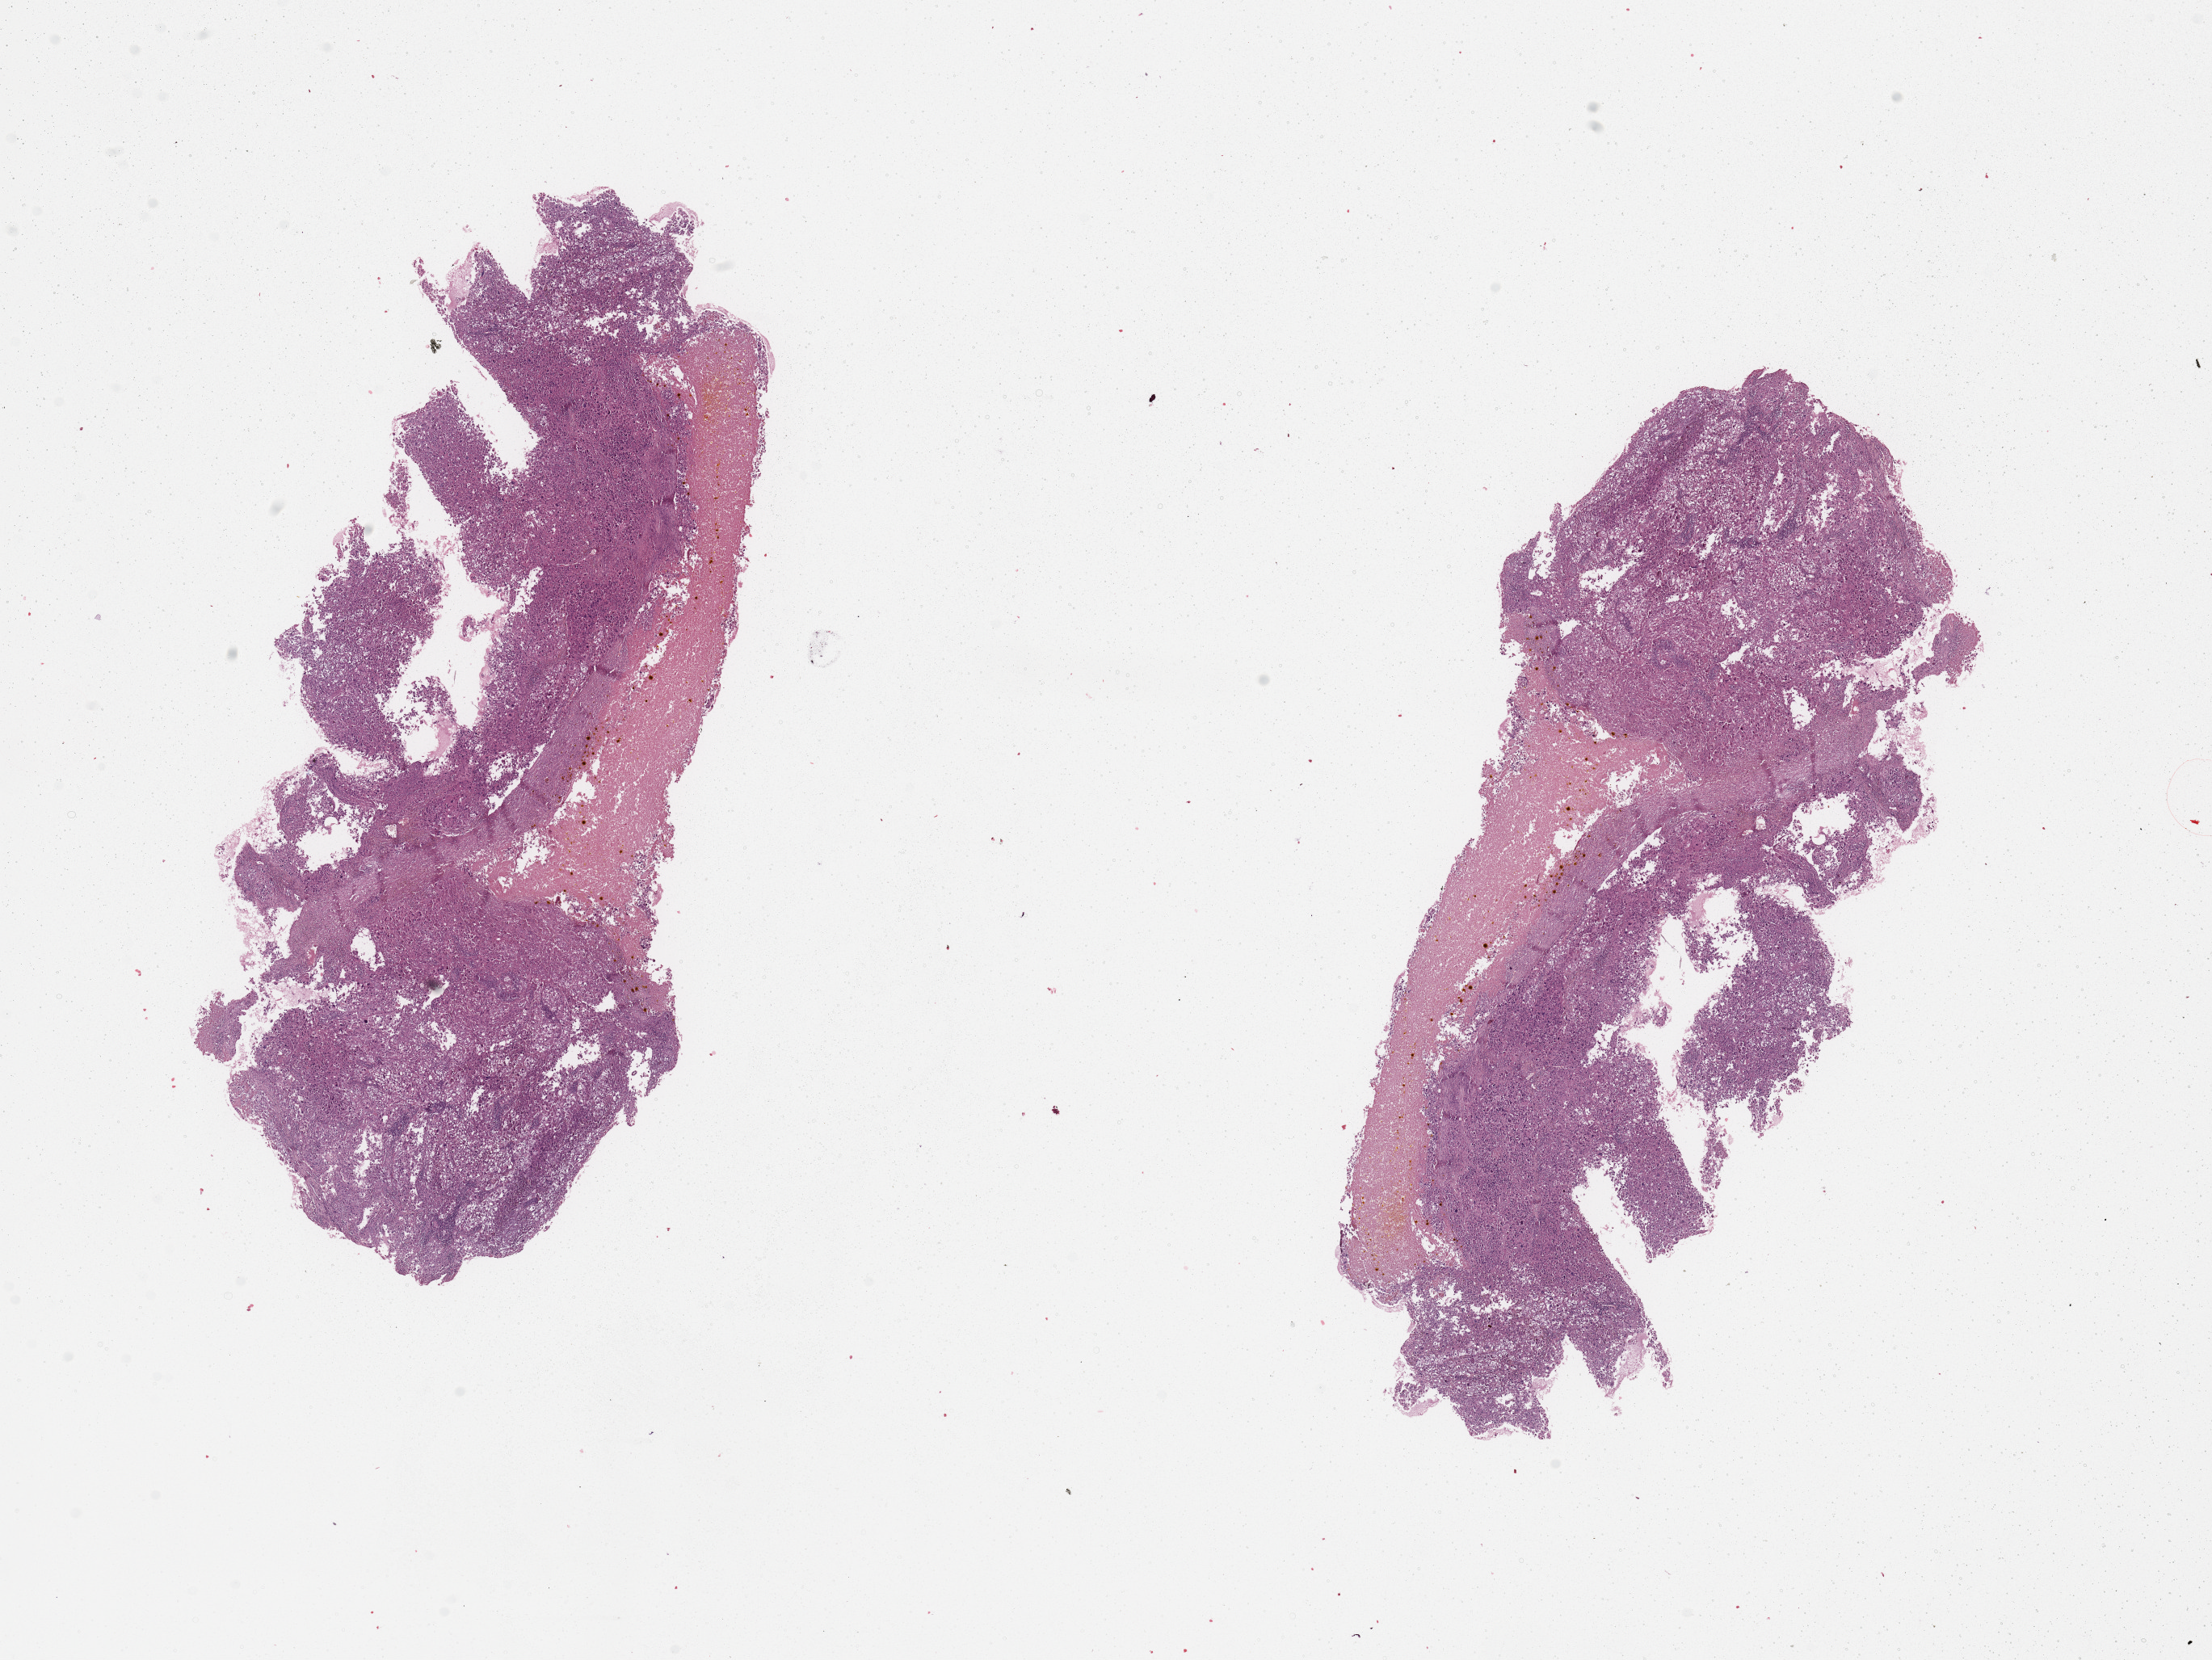
H&E-stained whole-slide image, low-resolution overview of the scanned area, about 21.7 x 16.3 mm, melanoma tumour tissue; sampled site not recorded. Patient: male, age 33 years.
• diagnosis: Malignant melanoma, NOS
• AJCC pathologic stage: IIC
• primary tumour site (as recorded): trunk